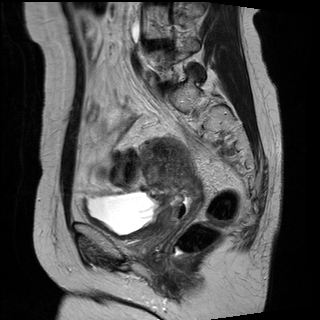
Pelvic MRI for cervical cancer, one sagittal slice; slice 10 of 27 in the series (ordered by position); T2-weighted; 1.5 T; TE 89 ms, TR 2740 ms; 320 × 320 image matrix, field of view 260 × 260 mm. Female patient, age 42 years.
Structures marked on this image (manually delineated by an expert):
- uterus and cervix: bounding box [x1, y1, x2, y2] px = [142, 137, 202, 228]